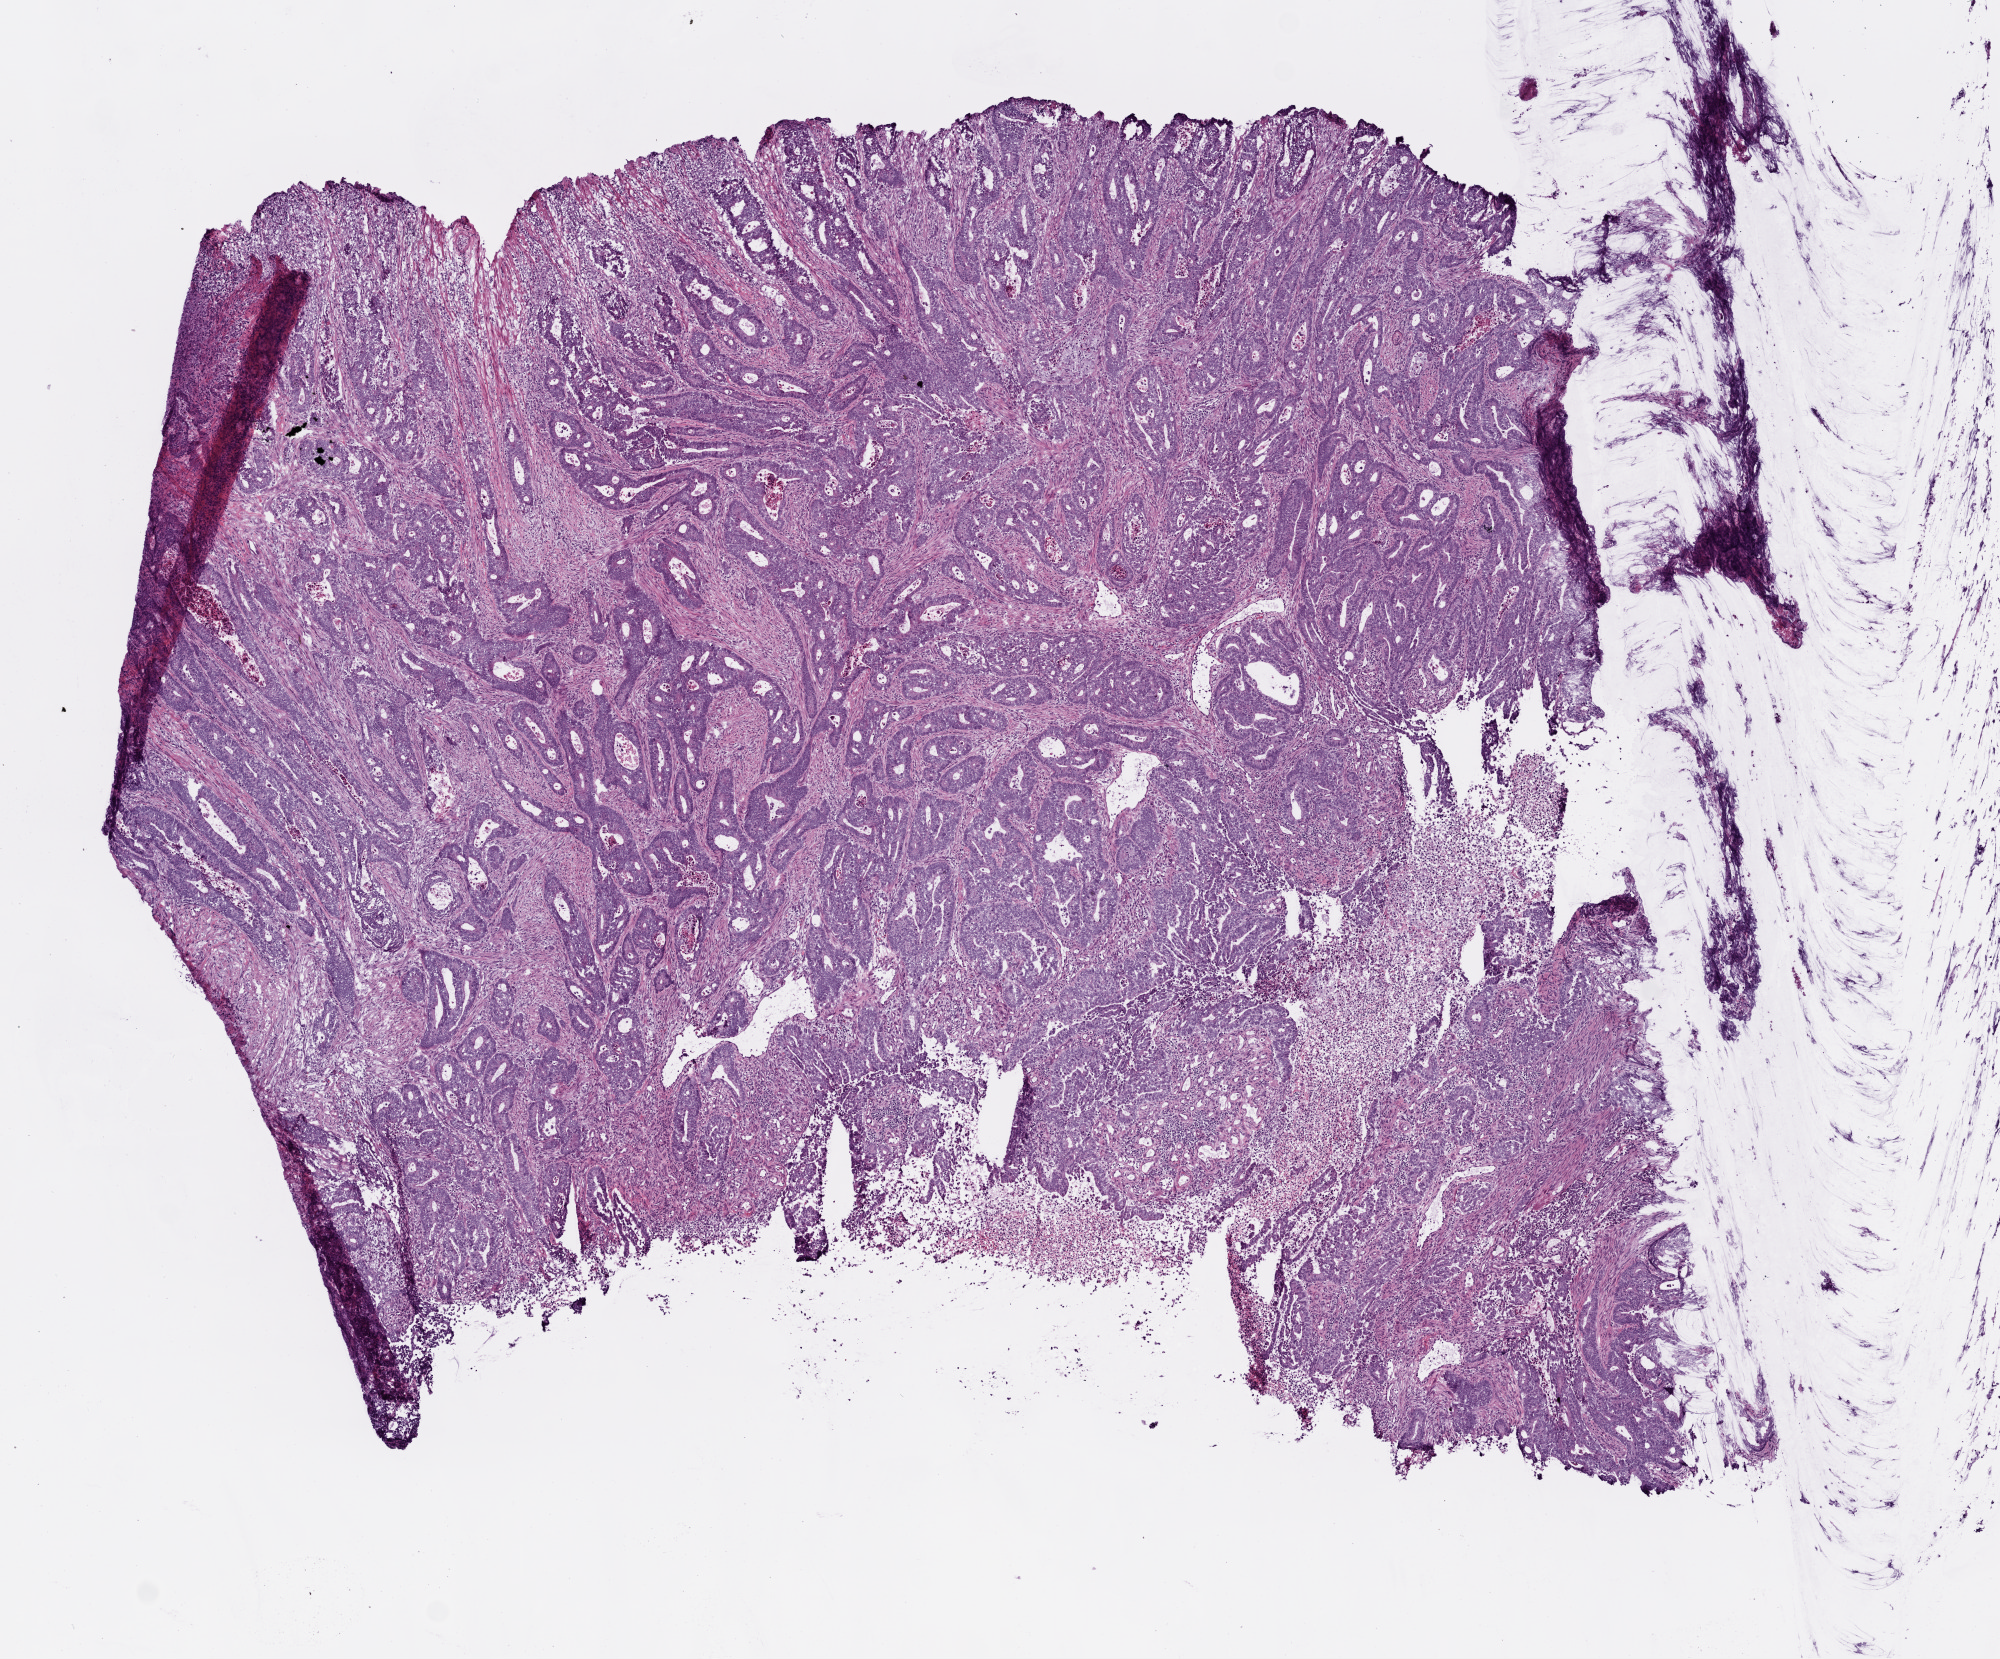
Whole-slide histology image, H&E — shown as a low-resolution overview of the whole scanned area (about 8.0 x 6.7 mm, slide scanned at 20x); frozen section from the top of the tissue portion; primary tumour sample from the colon. Male patient; age at initial diagnosis 73 years. Pathologist review of this section (percent, as recorded): tumour cells 95%, tumour nuclei 80%, normal cells 0%, stromal cells 0%, necrosis 5%. Inflammatory infiltration, as recorded: lymphocyte infiltration 10%, monocyte infiltration 1%, neutrophil infiltration 2%.
Lymph nodes positive (case pathology): 0 of 12 examined. Histologic diagnosis: Adenocarcinoma, NOS. AJCC pathologic stage: IIA.